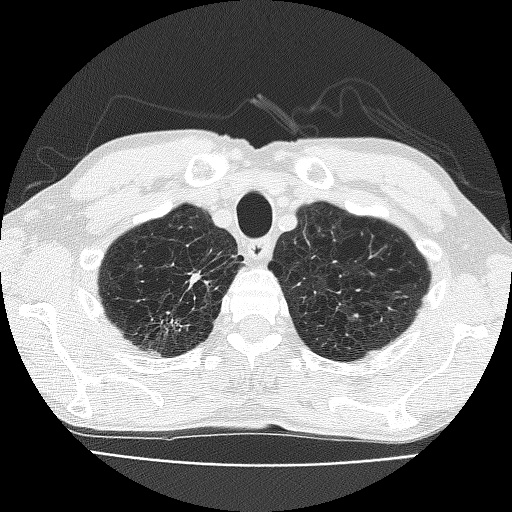
Low-dose screening chest CT, one axial slice; position 153 of 185 along the scan axis; reconstruction kernel FC51; lung window (W 1500 / L -600 HU); 2 mm slice thickness; 512 × 512 image matrix, field of view 322 × 322 mm.
Annotated regions visible in this slice (outlined manually by an expert reader):
- lesion 1 (nodule, upper lobe of right lung): bounding box [x1, y1, x2, y2] px = [190, 273, 200, 285]